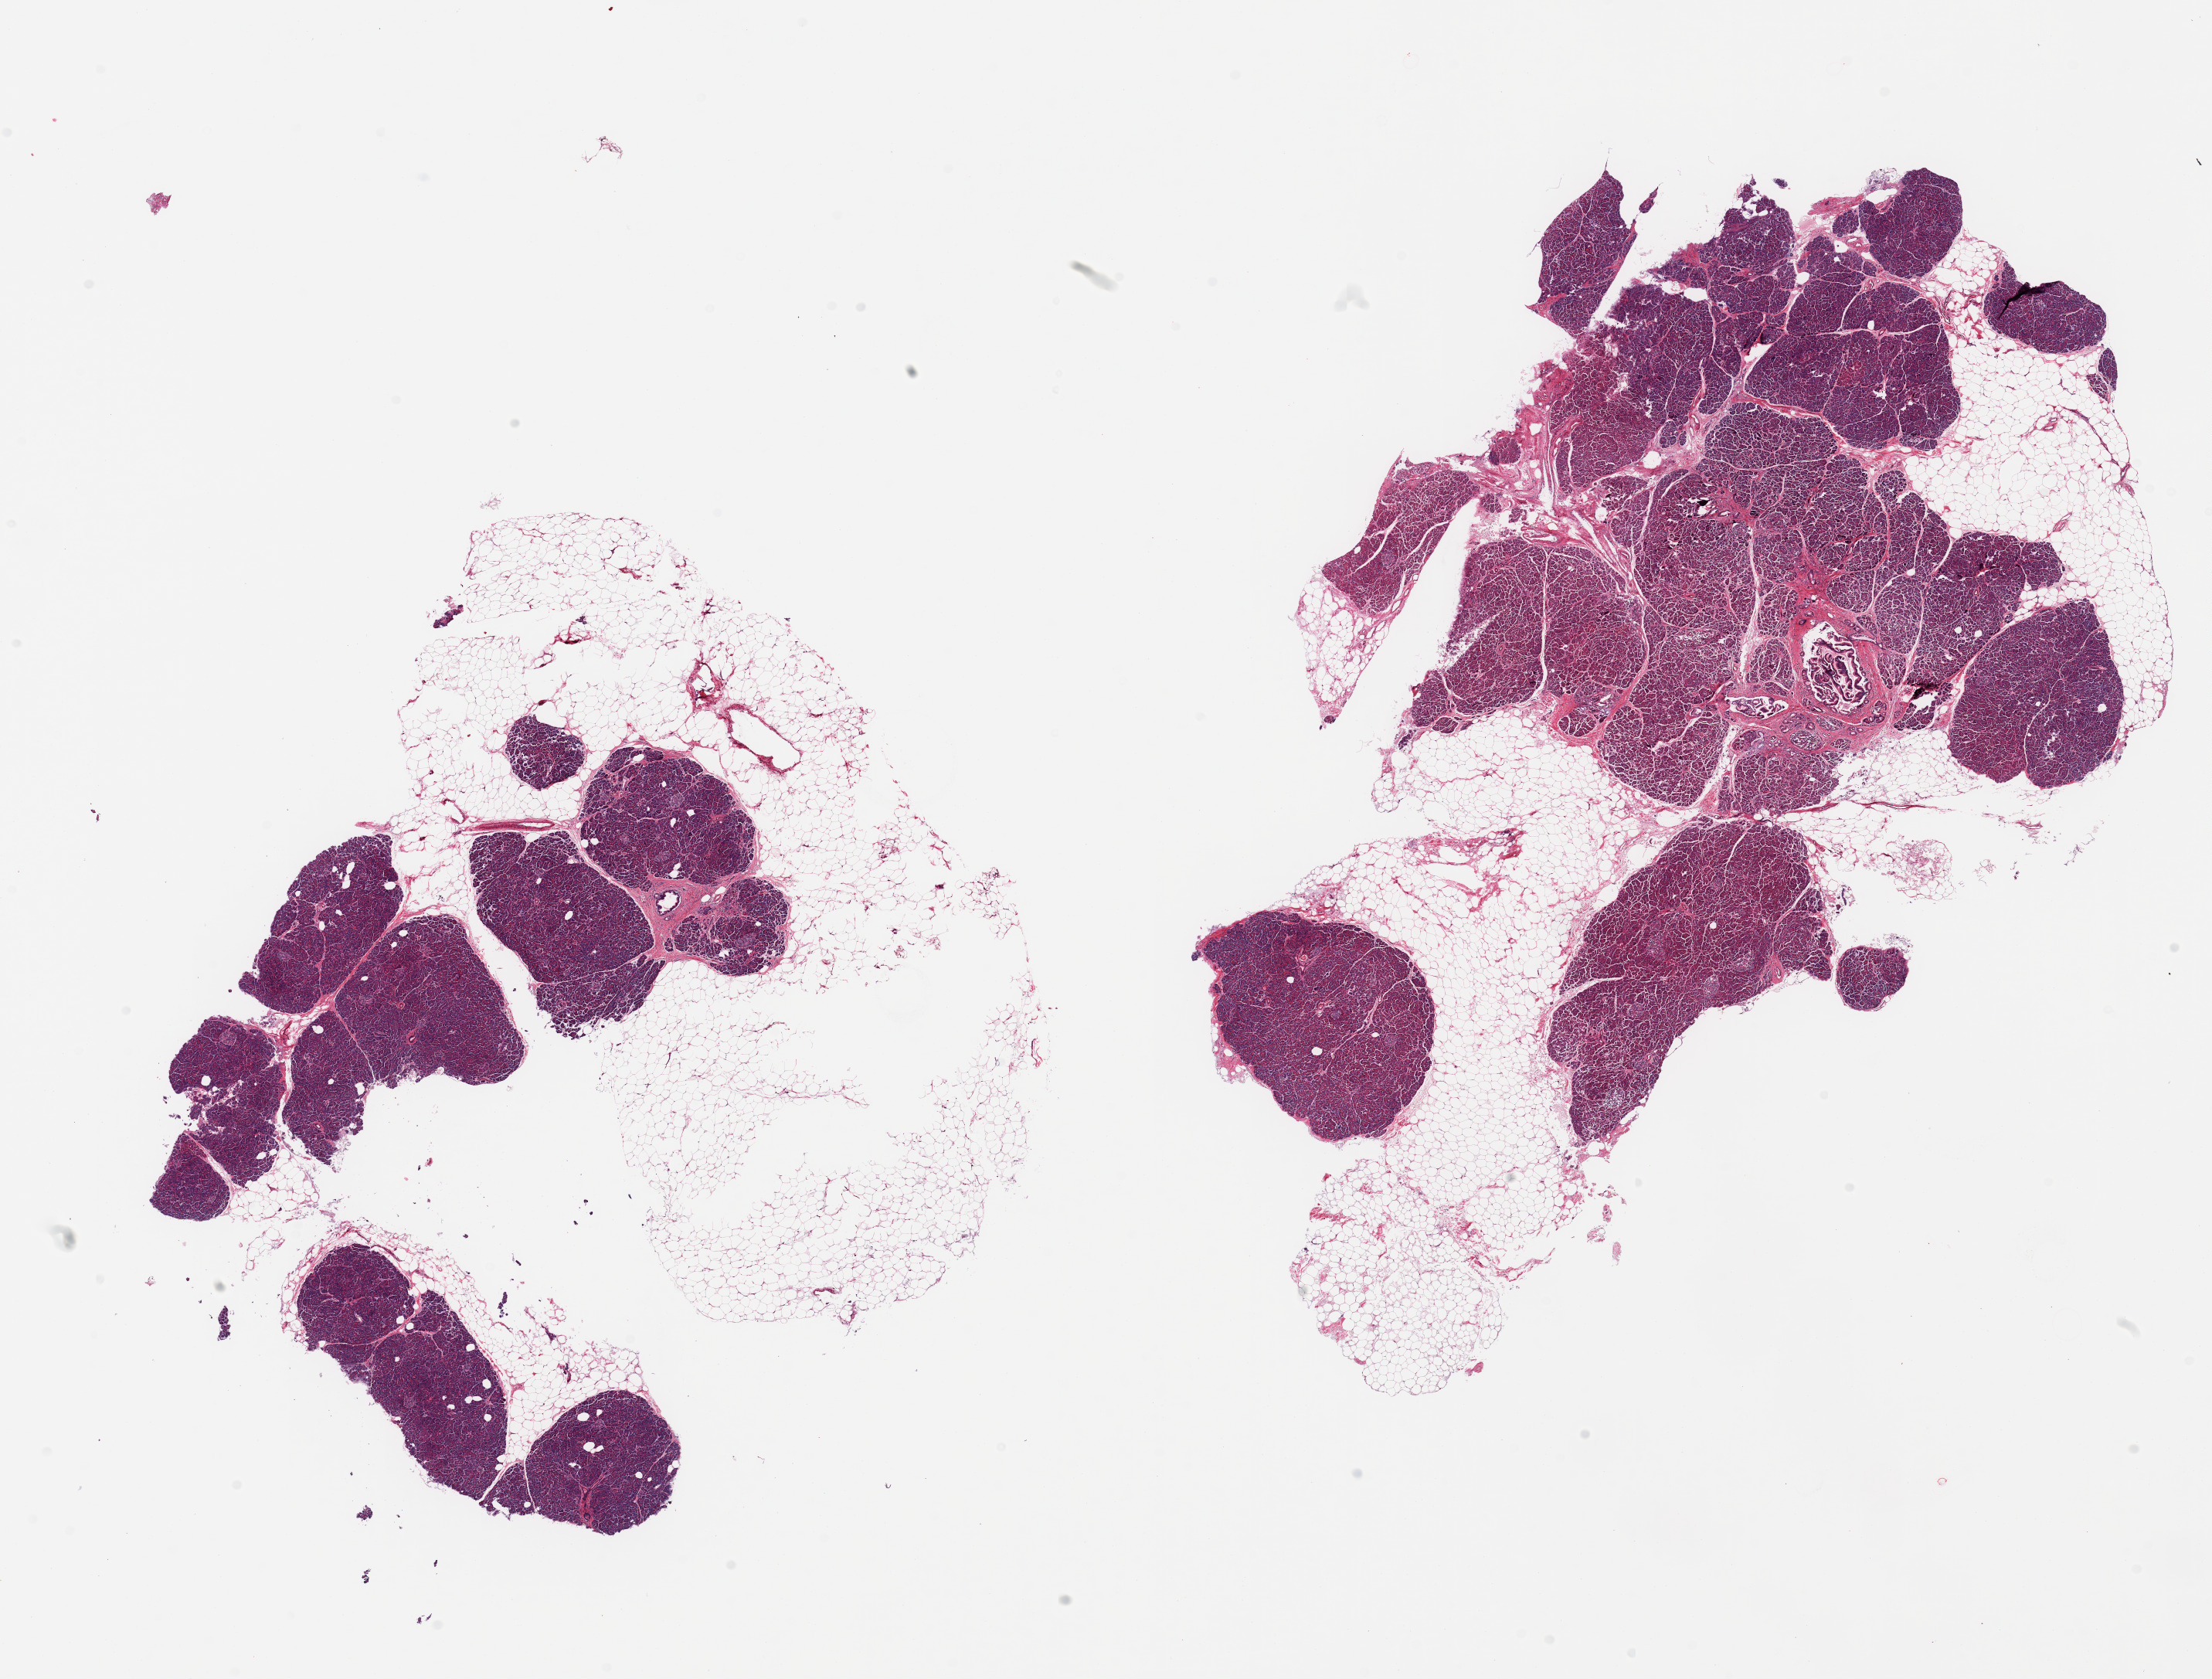
Digitized H&E-stained section, brightfield — a low-resolution overview of the entire scanned area, about 22.6 x 17.2 mm. PAXgene-fixed, paraffin-embedded tissue. Target tissue: pancreas. Donor tissue sample. Male donor.
Reviewer comment on this tissue sample: 2 pieces; 40 and 50% fat.